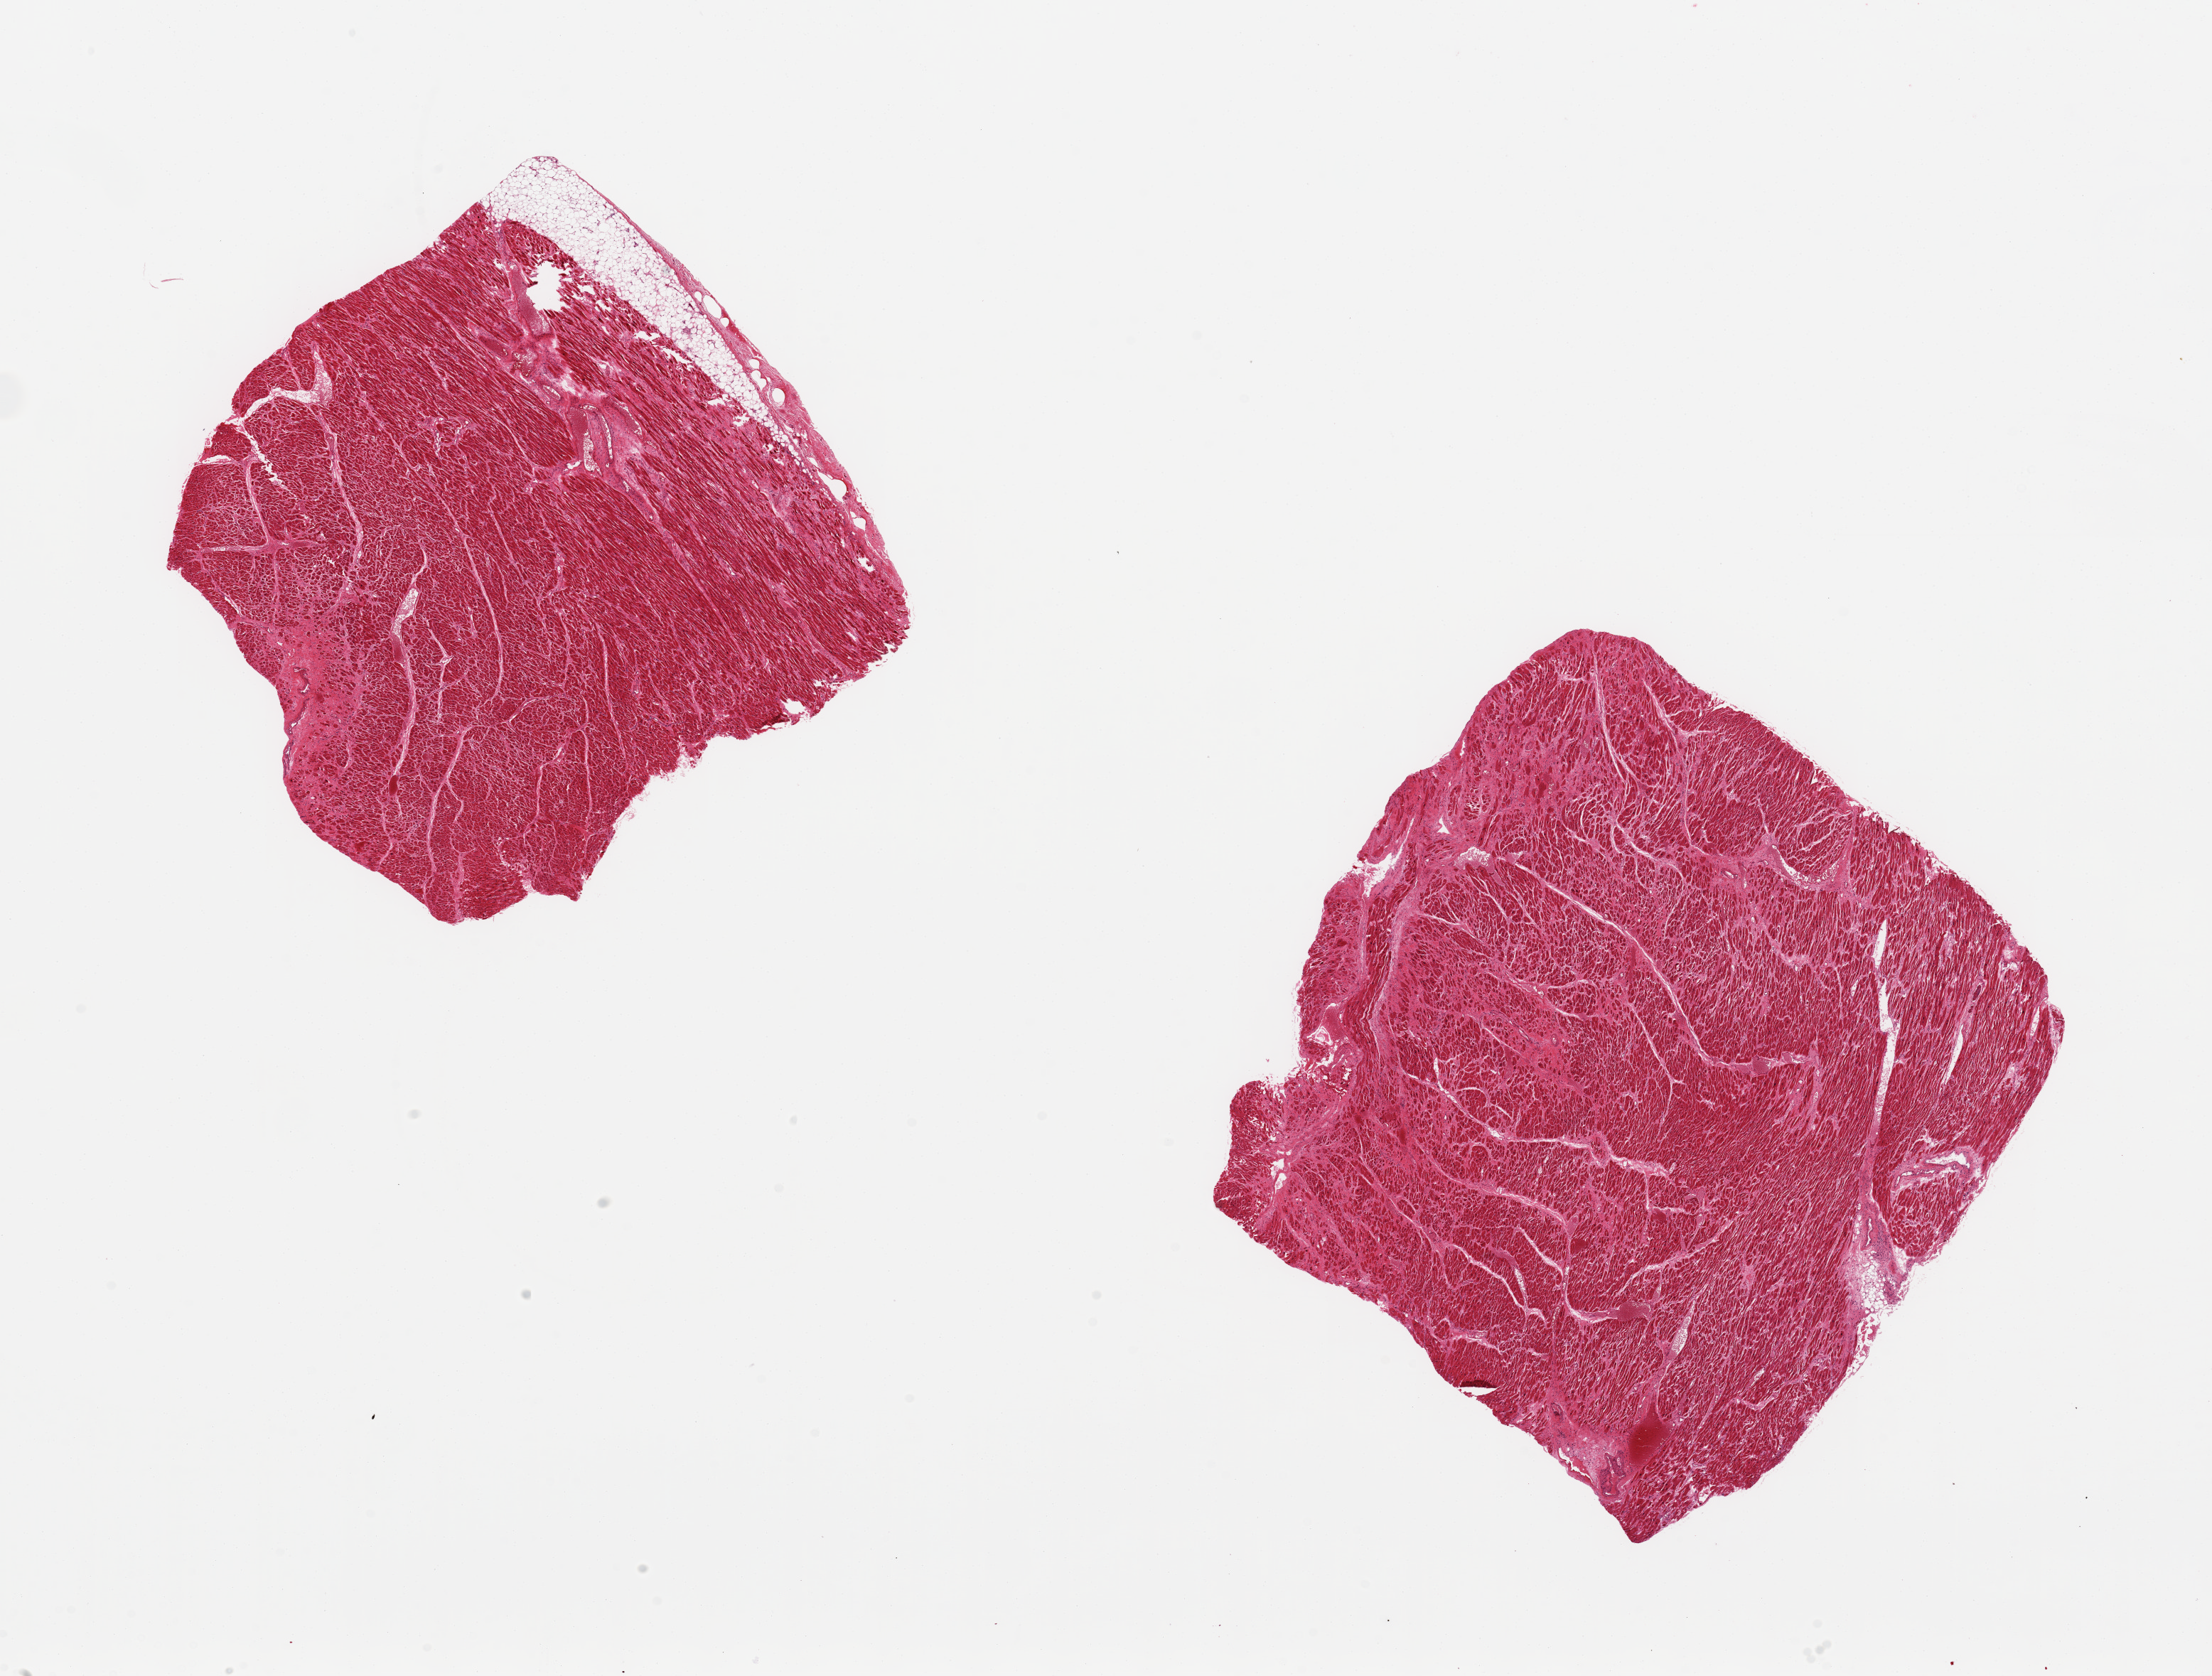
Digitized hematoxylin and eosin (H&E)-stained section, brightfield — whole scanned area (about 24.6 x 18.6 mm) shown as a low-resolution overview. PAXgene-fixed, paraffin-embedded tissue. Target tissue: heart. Donor tissue sample.
Pathologist's review note for this sample: 2 ~7x6mm pieces. Diffuse fibrosis, evidence of subacute infarct.